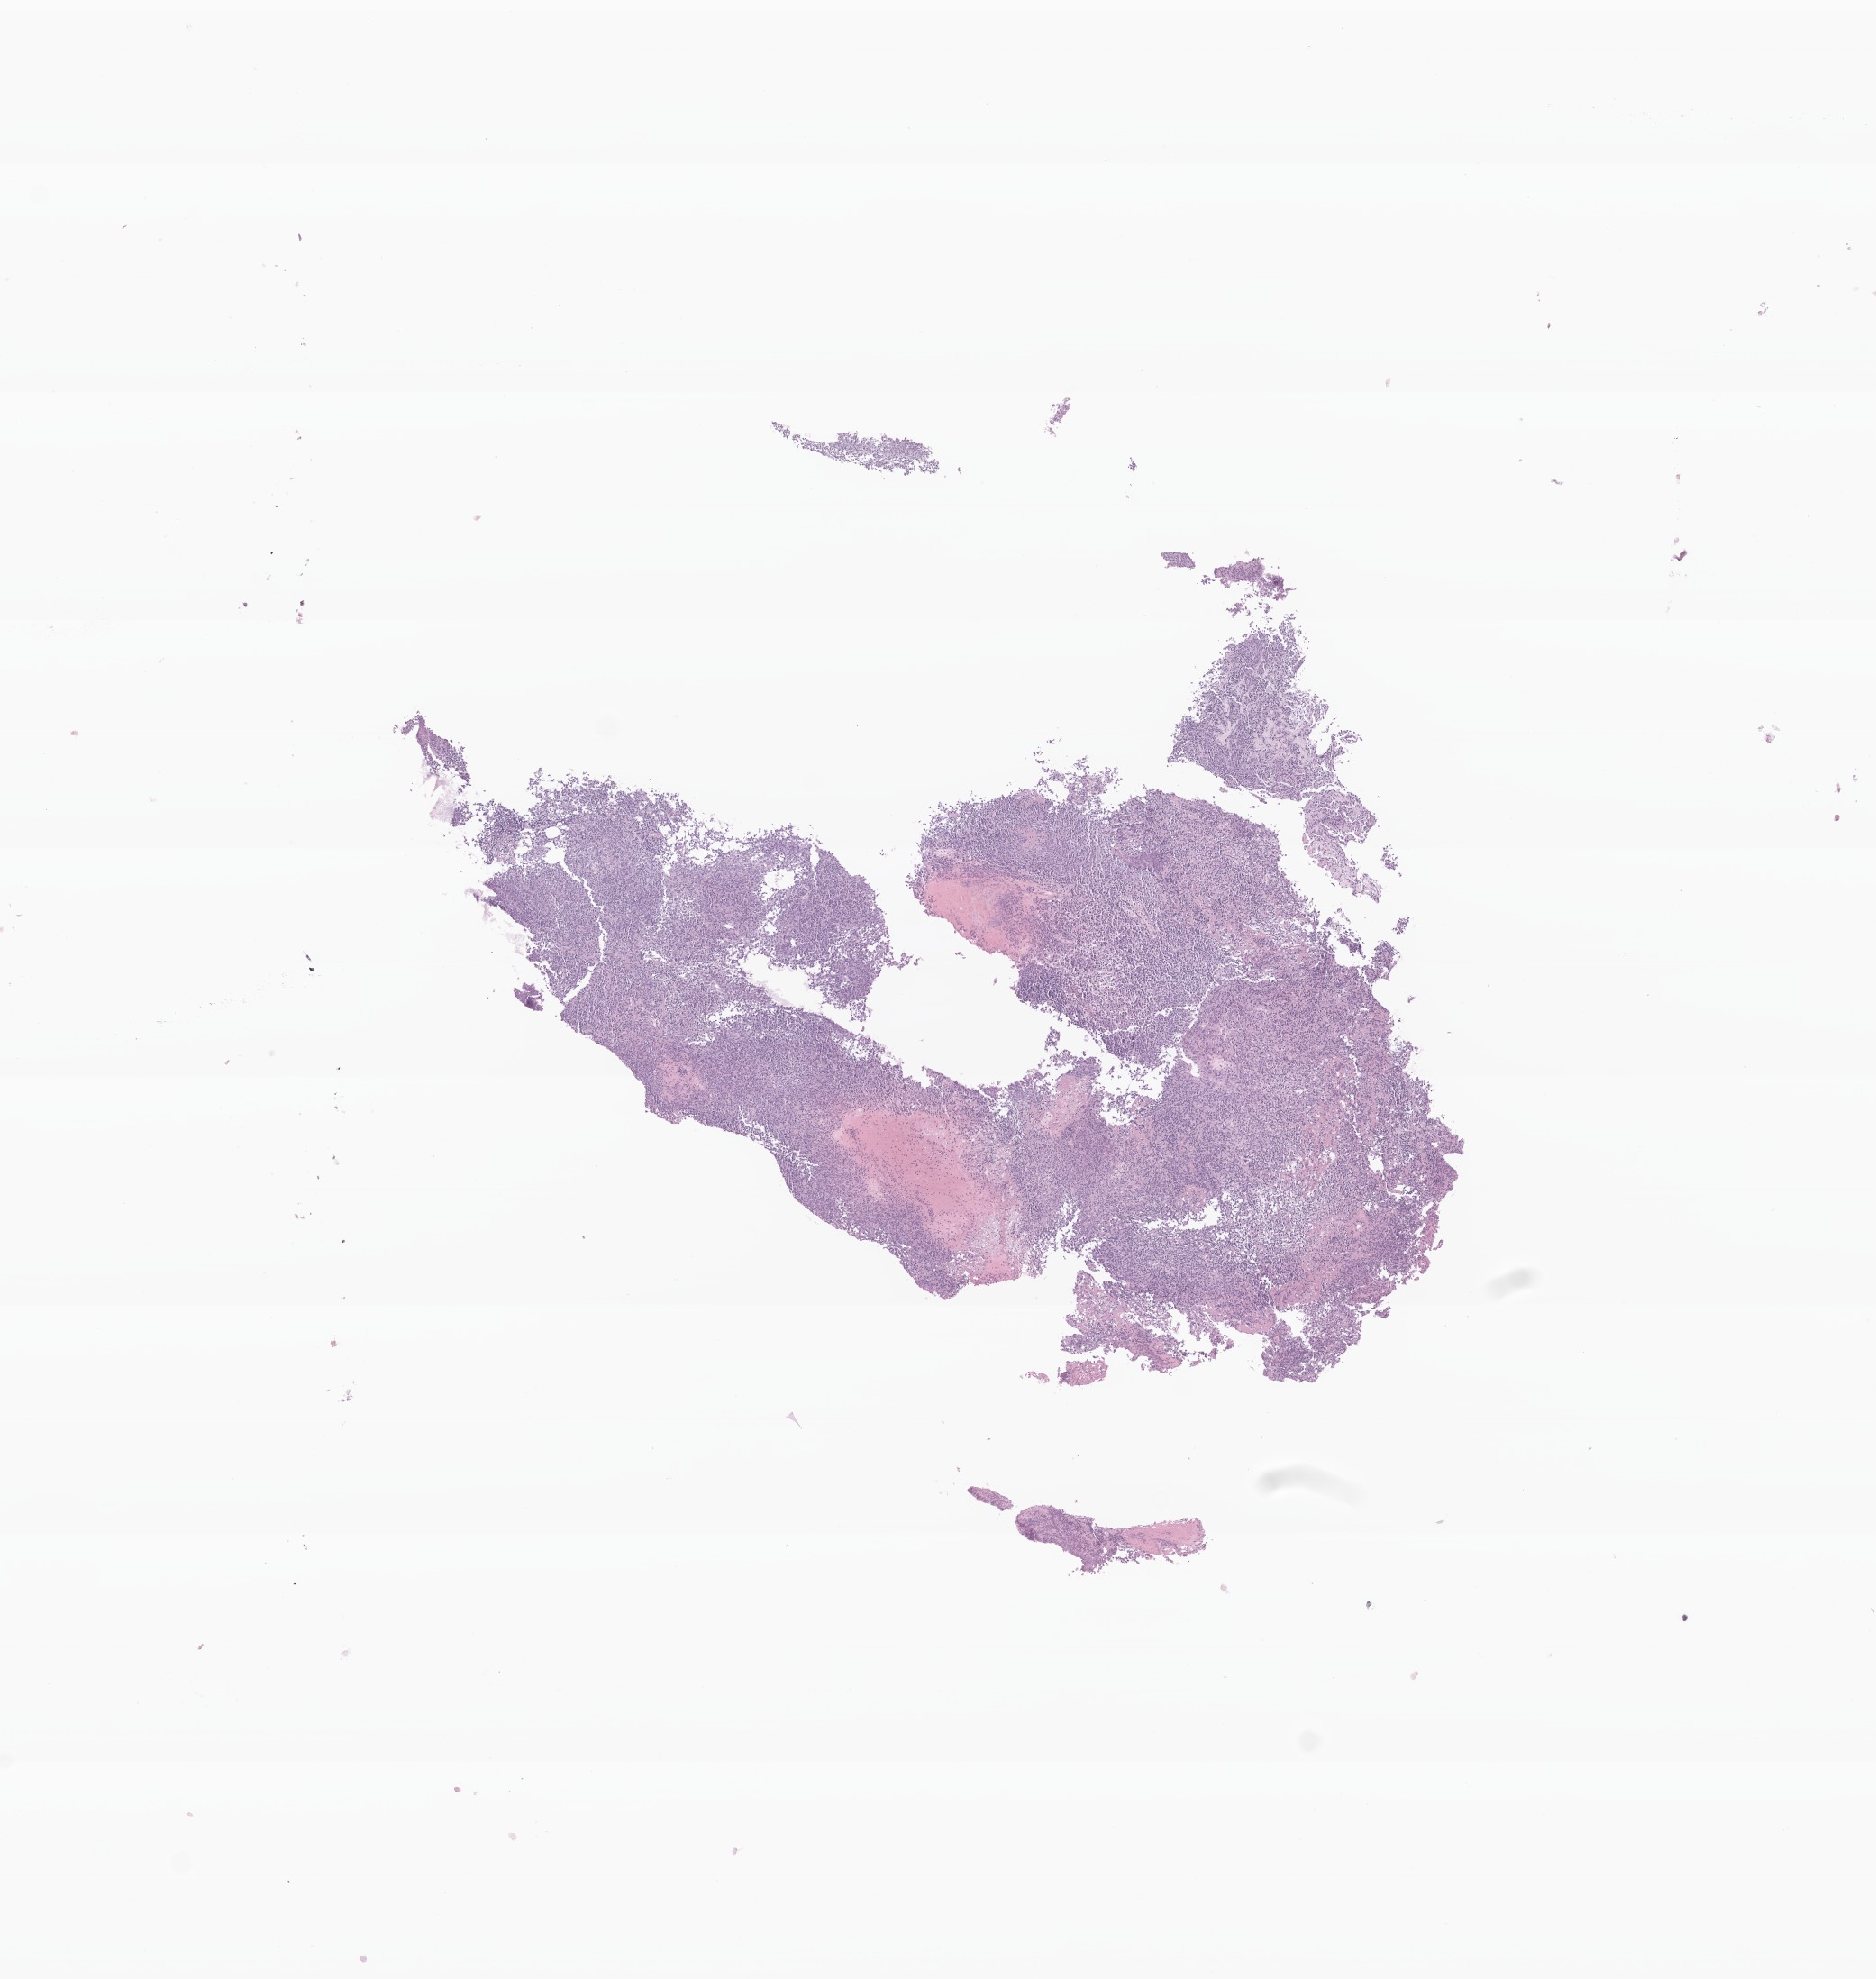
Whole-slide image, haematoxylin and eosin stain of tumor tissue from the spinal cord, shown as a low-resolution overview of the whole scanned area (about 8.8 x 9.2 mm). Formalin-fixed, paraffin-embedded (FFPE) tissue. Patient male; age 34 months (2 years 10 months).
Diagnosis: Atypical teratoid/rhabdoid tumor.